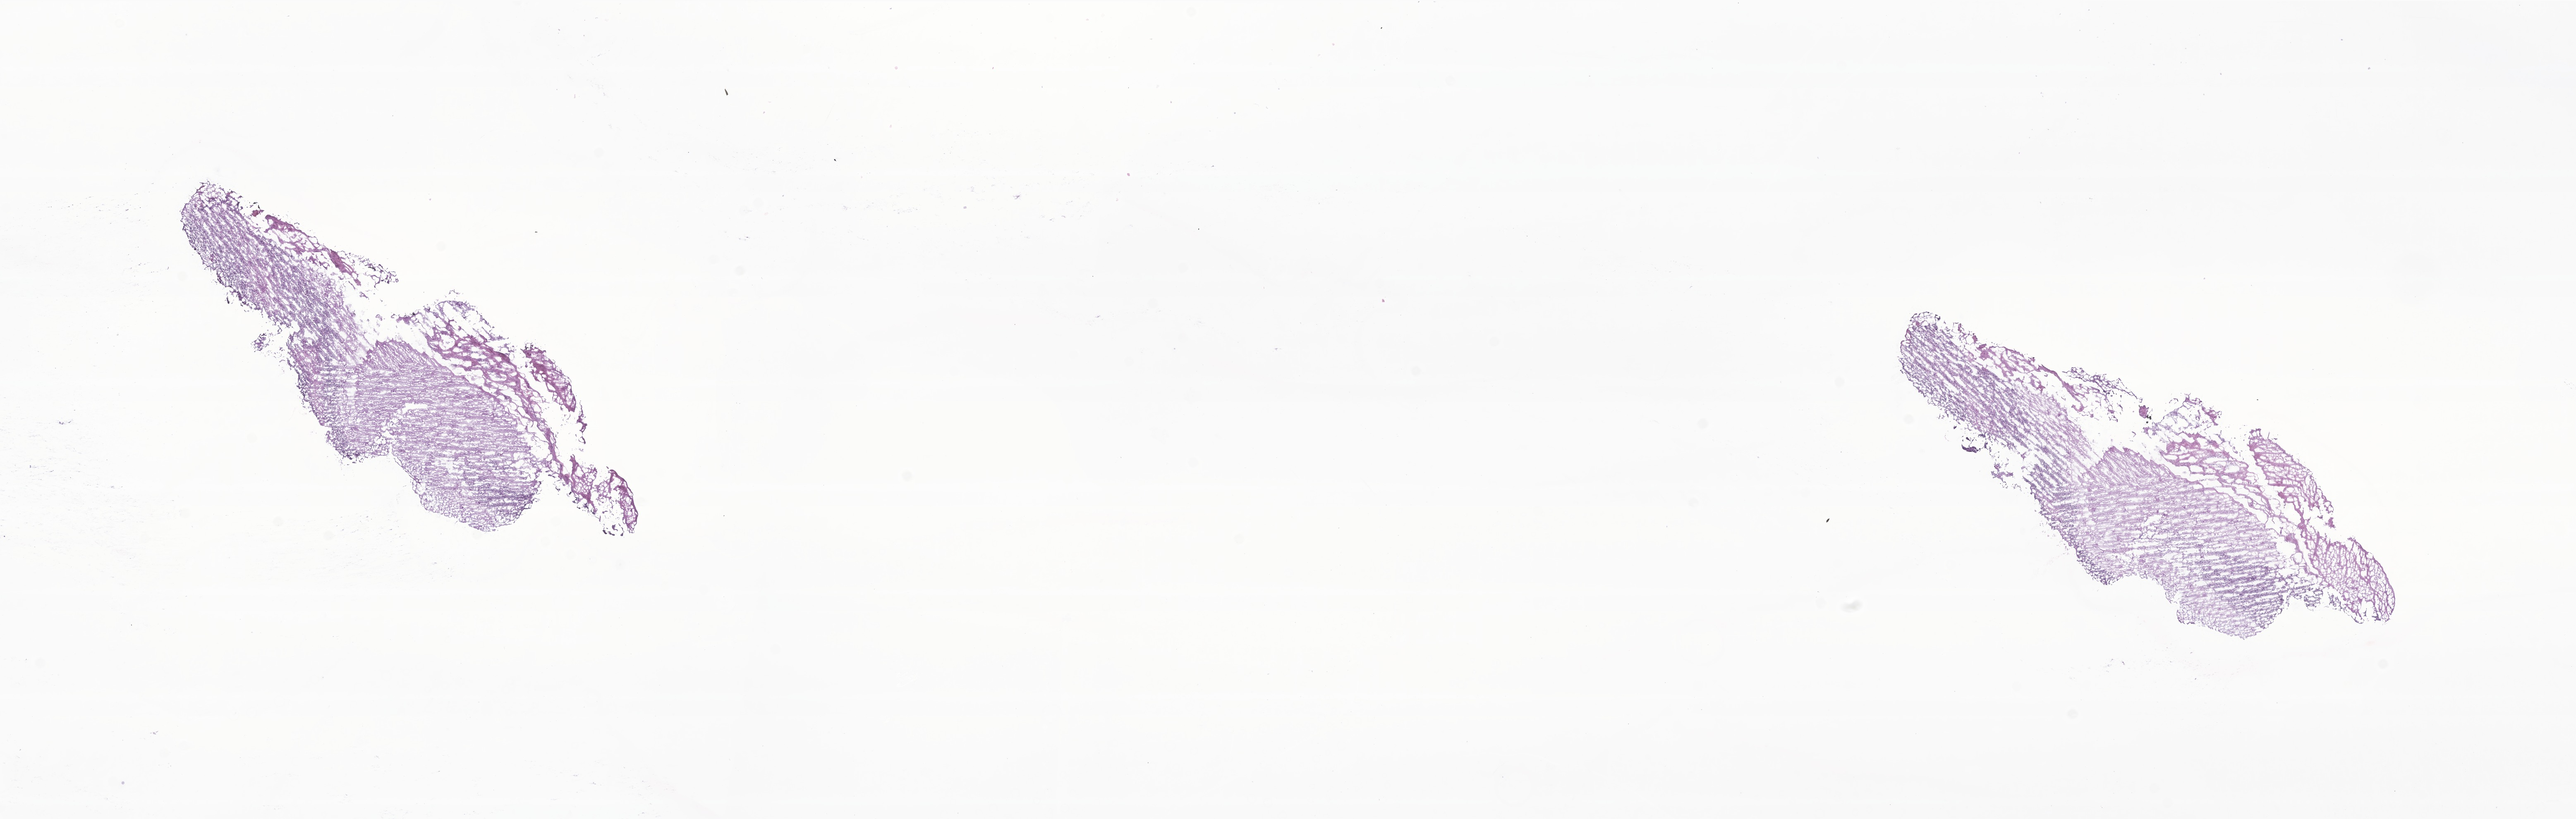
Digitized H&E-stained section of tumor tissue from the brain — a low-resolution overview of the entire scanned area, about 26.3 x 8.4 mm, cryosection (OCT / tissue freezing medium). Patient male; age 51 months (4 years 3 months).
Recorded diagnosis: Pilocytic astrocytoma.